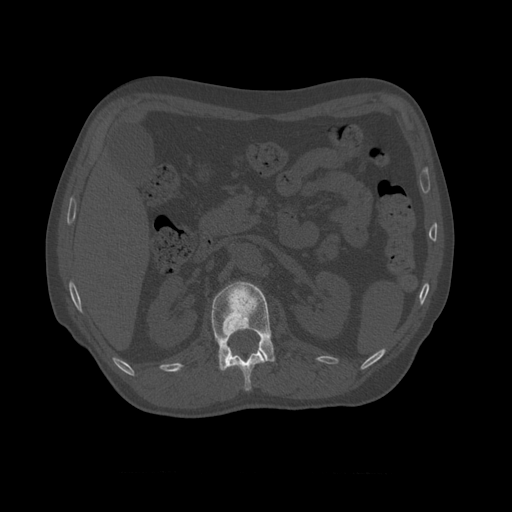
CT including the spine, one axial slice; position 363 of 450 along the scan axis; reconstruction kernel STANDARD; bone window (W 1800 / L 400 HU); 512 × 512 image matrix, field of view 405 × 405 mm. Patient age 75 years. Case-level facts recorded for this patient, not image findings: primary cancer: prostate.
Outlined on this slice (semi-automatically segmented with operator editing):
- L1 vertebra: box from (x=211, y=281) to (x=276, y=372) px
- T10 vertebra: (x=222, y=345)–(x=268, y=371)
- T11 vertebra: (x=226, y=349)–(x=268, y=392)